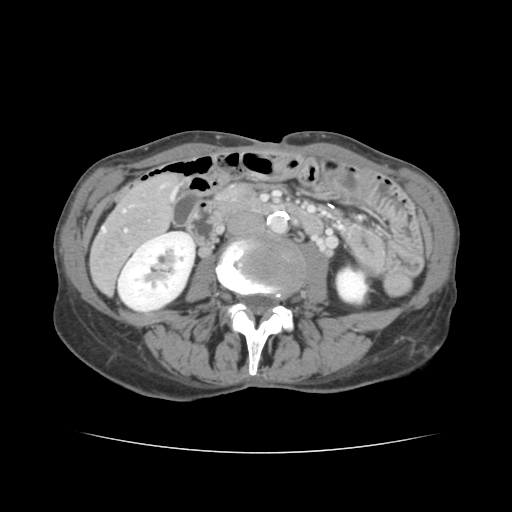
Contrast-enhanced abdominal CT, one axial slice. Position 37 of 136 along the scan axis. Intravenous contrast given. Soft-tissue window (W 400 / L 40 HU). 2.5 mm slice thickness. 512 × 512 image matrix. Female patient, age 77 years. Case-level facts recorded for this patient, not image findings: diagnosis: colorectal cancer liver metastases, imaged before liver resection; multiple liver metastases: yes.
Annotated regions visible in this slice (outlined manually by an expert reader):
- hepatic veins: box from (x=103, y=210) to (x=125, y=232) px
- liver: (x=91, y=176)–(x=179, y=291)